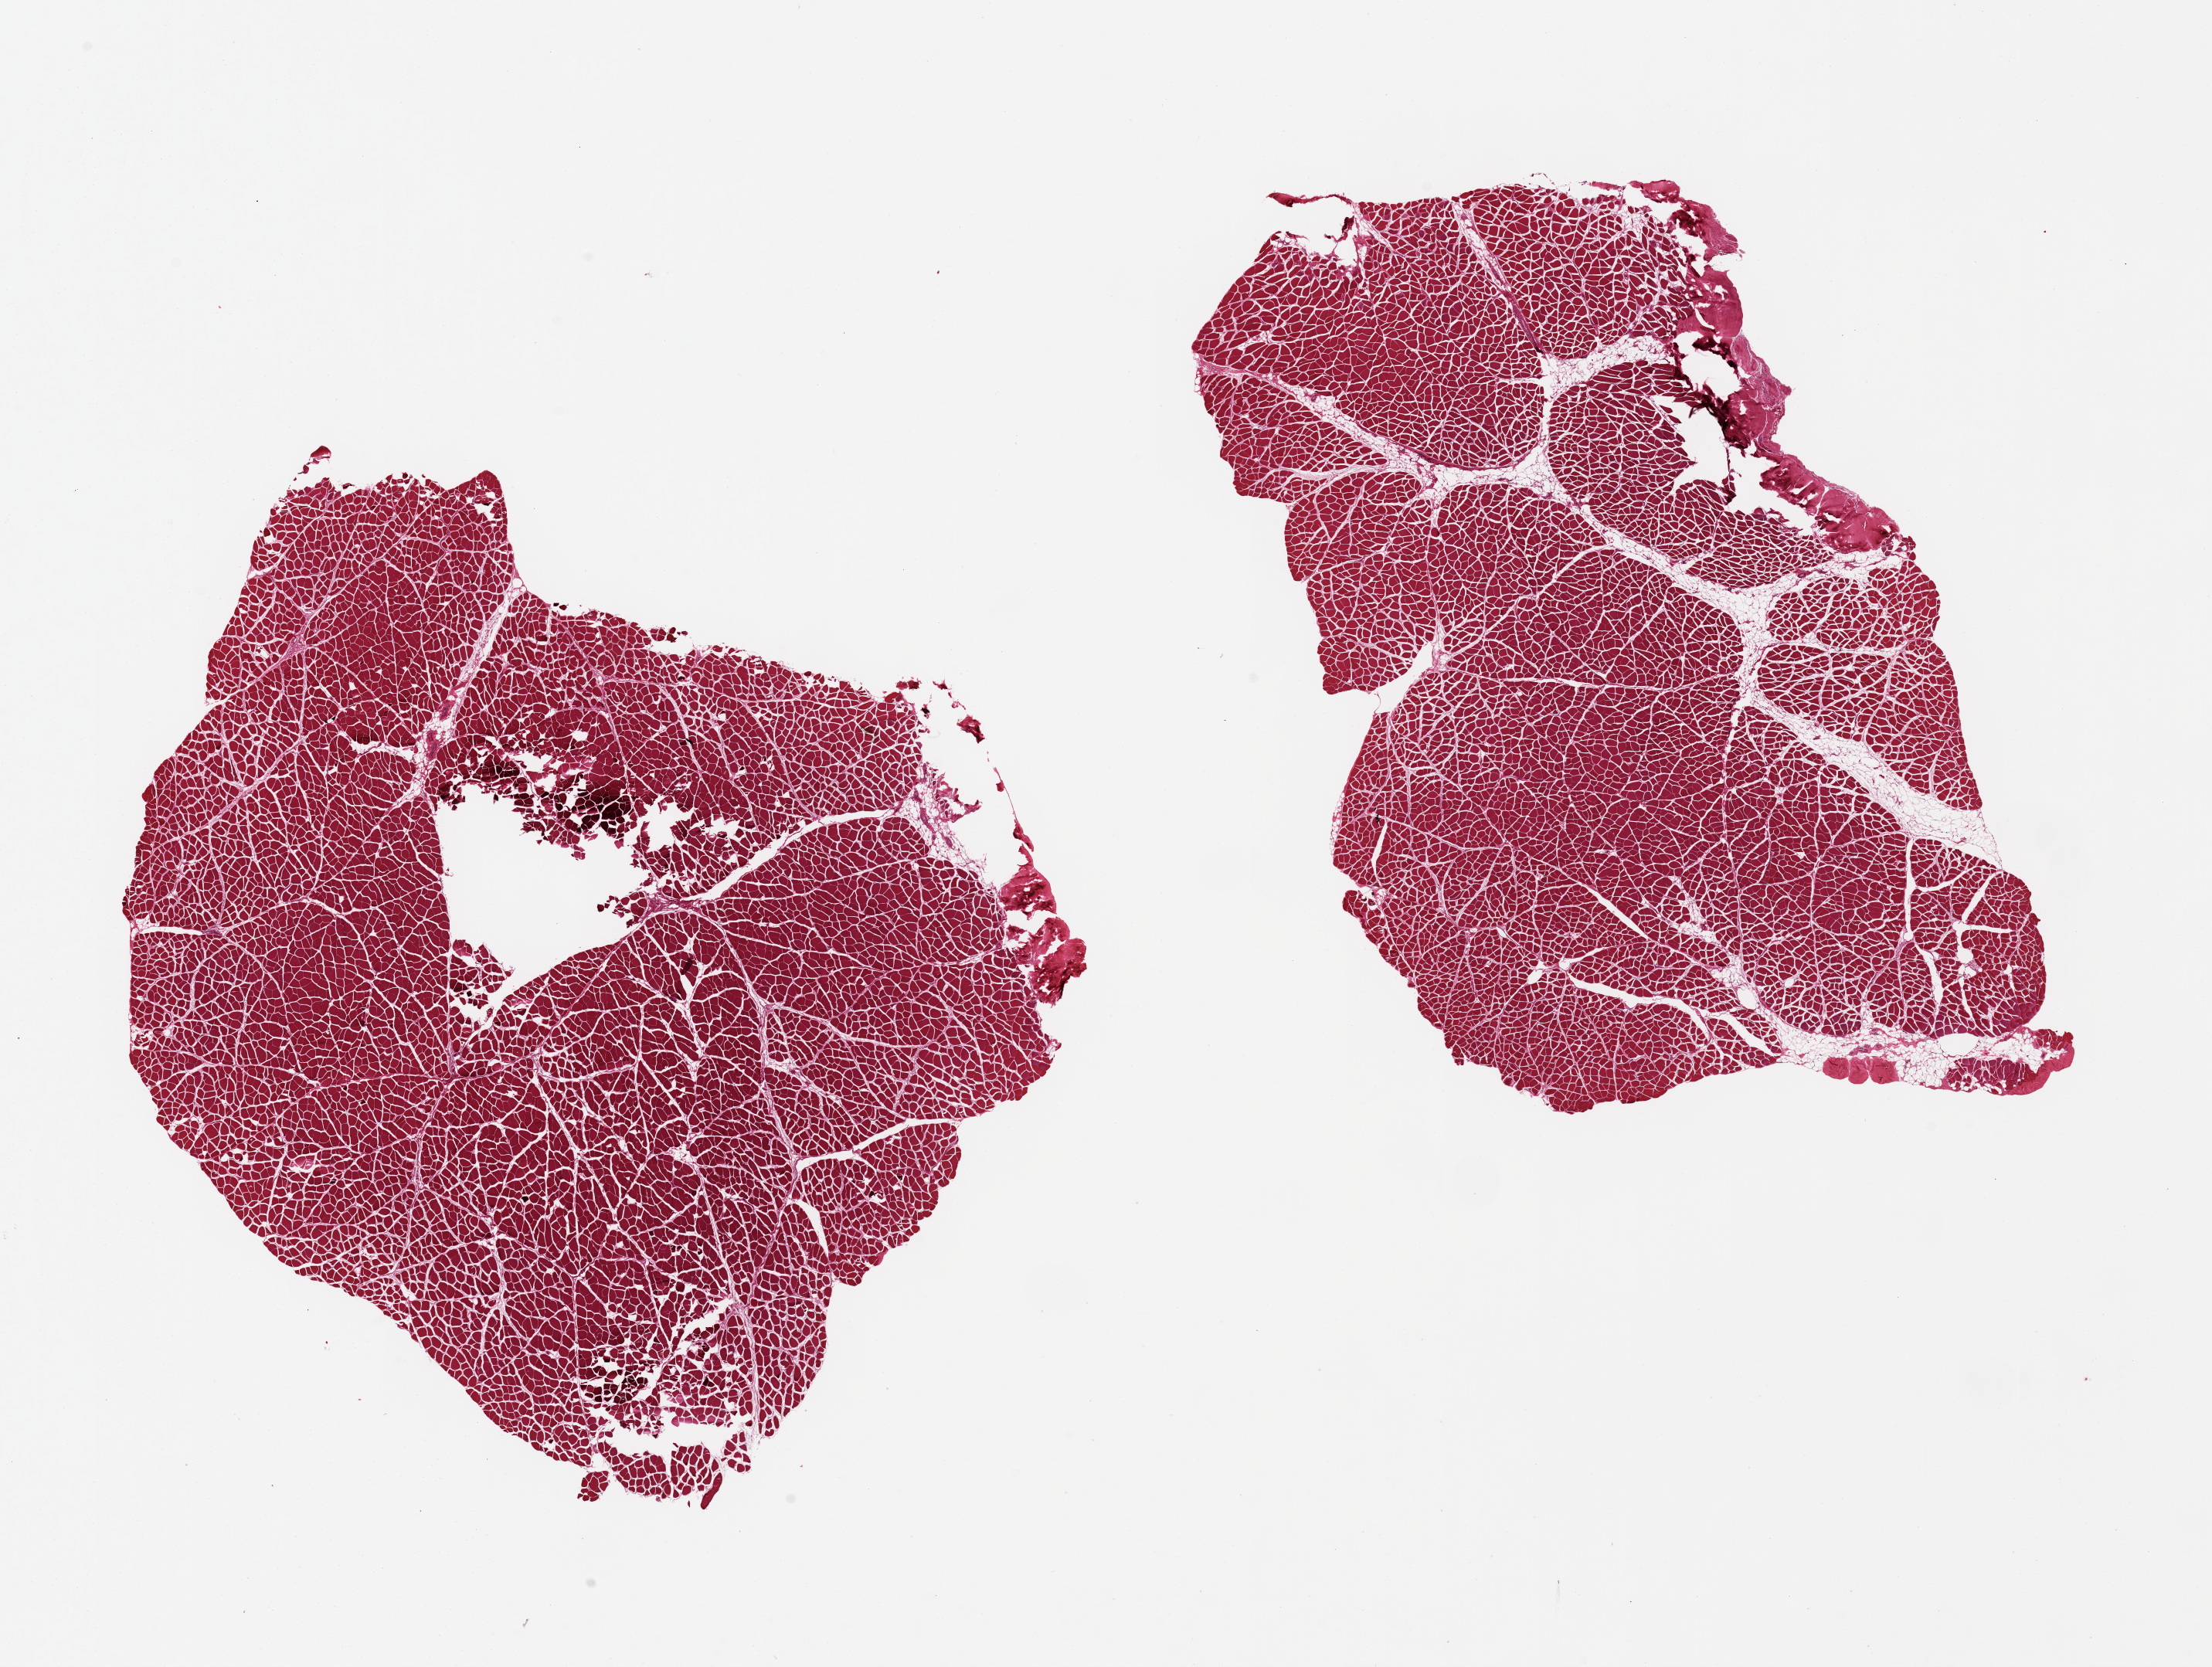
Hematoxylin and eosin (H&E) whole-slide image — a low-resolution overview of the entire scanned area, about 22.6 x 17.1 mm, PAXgene-fixed paraffin-embedded (PFPE) section, section of skeletal muscle (target tissue), tissue donor sample. Donor sex: female.
* review note (as recorded): 2 pieces, 11x9 & 9x6 mm; minimal adipose interspersed